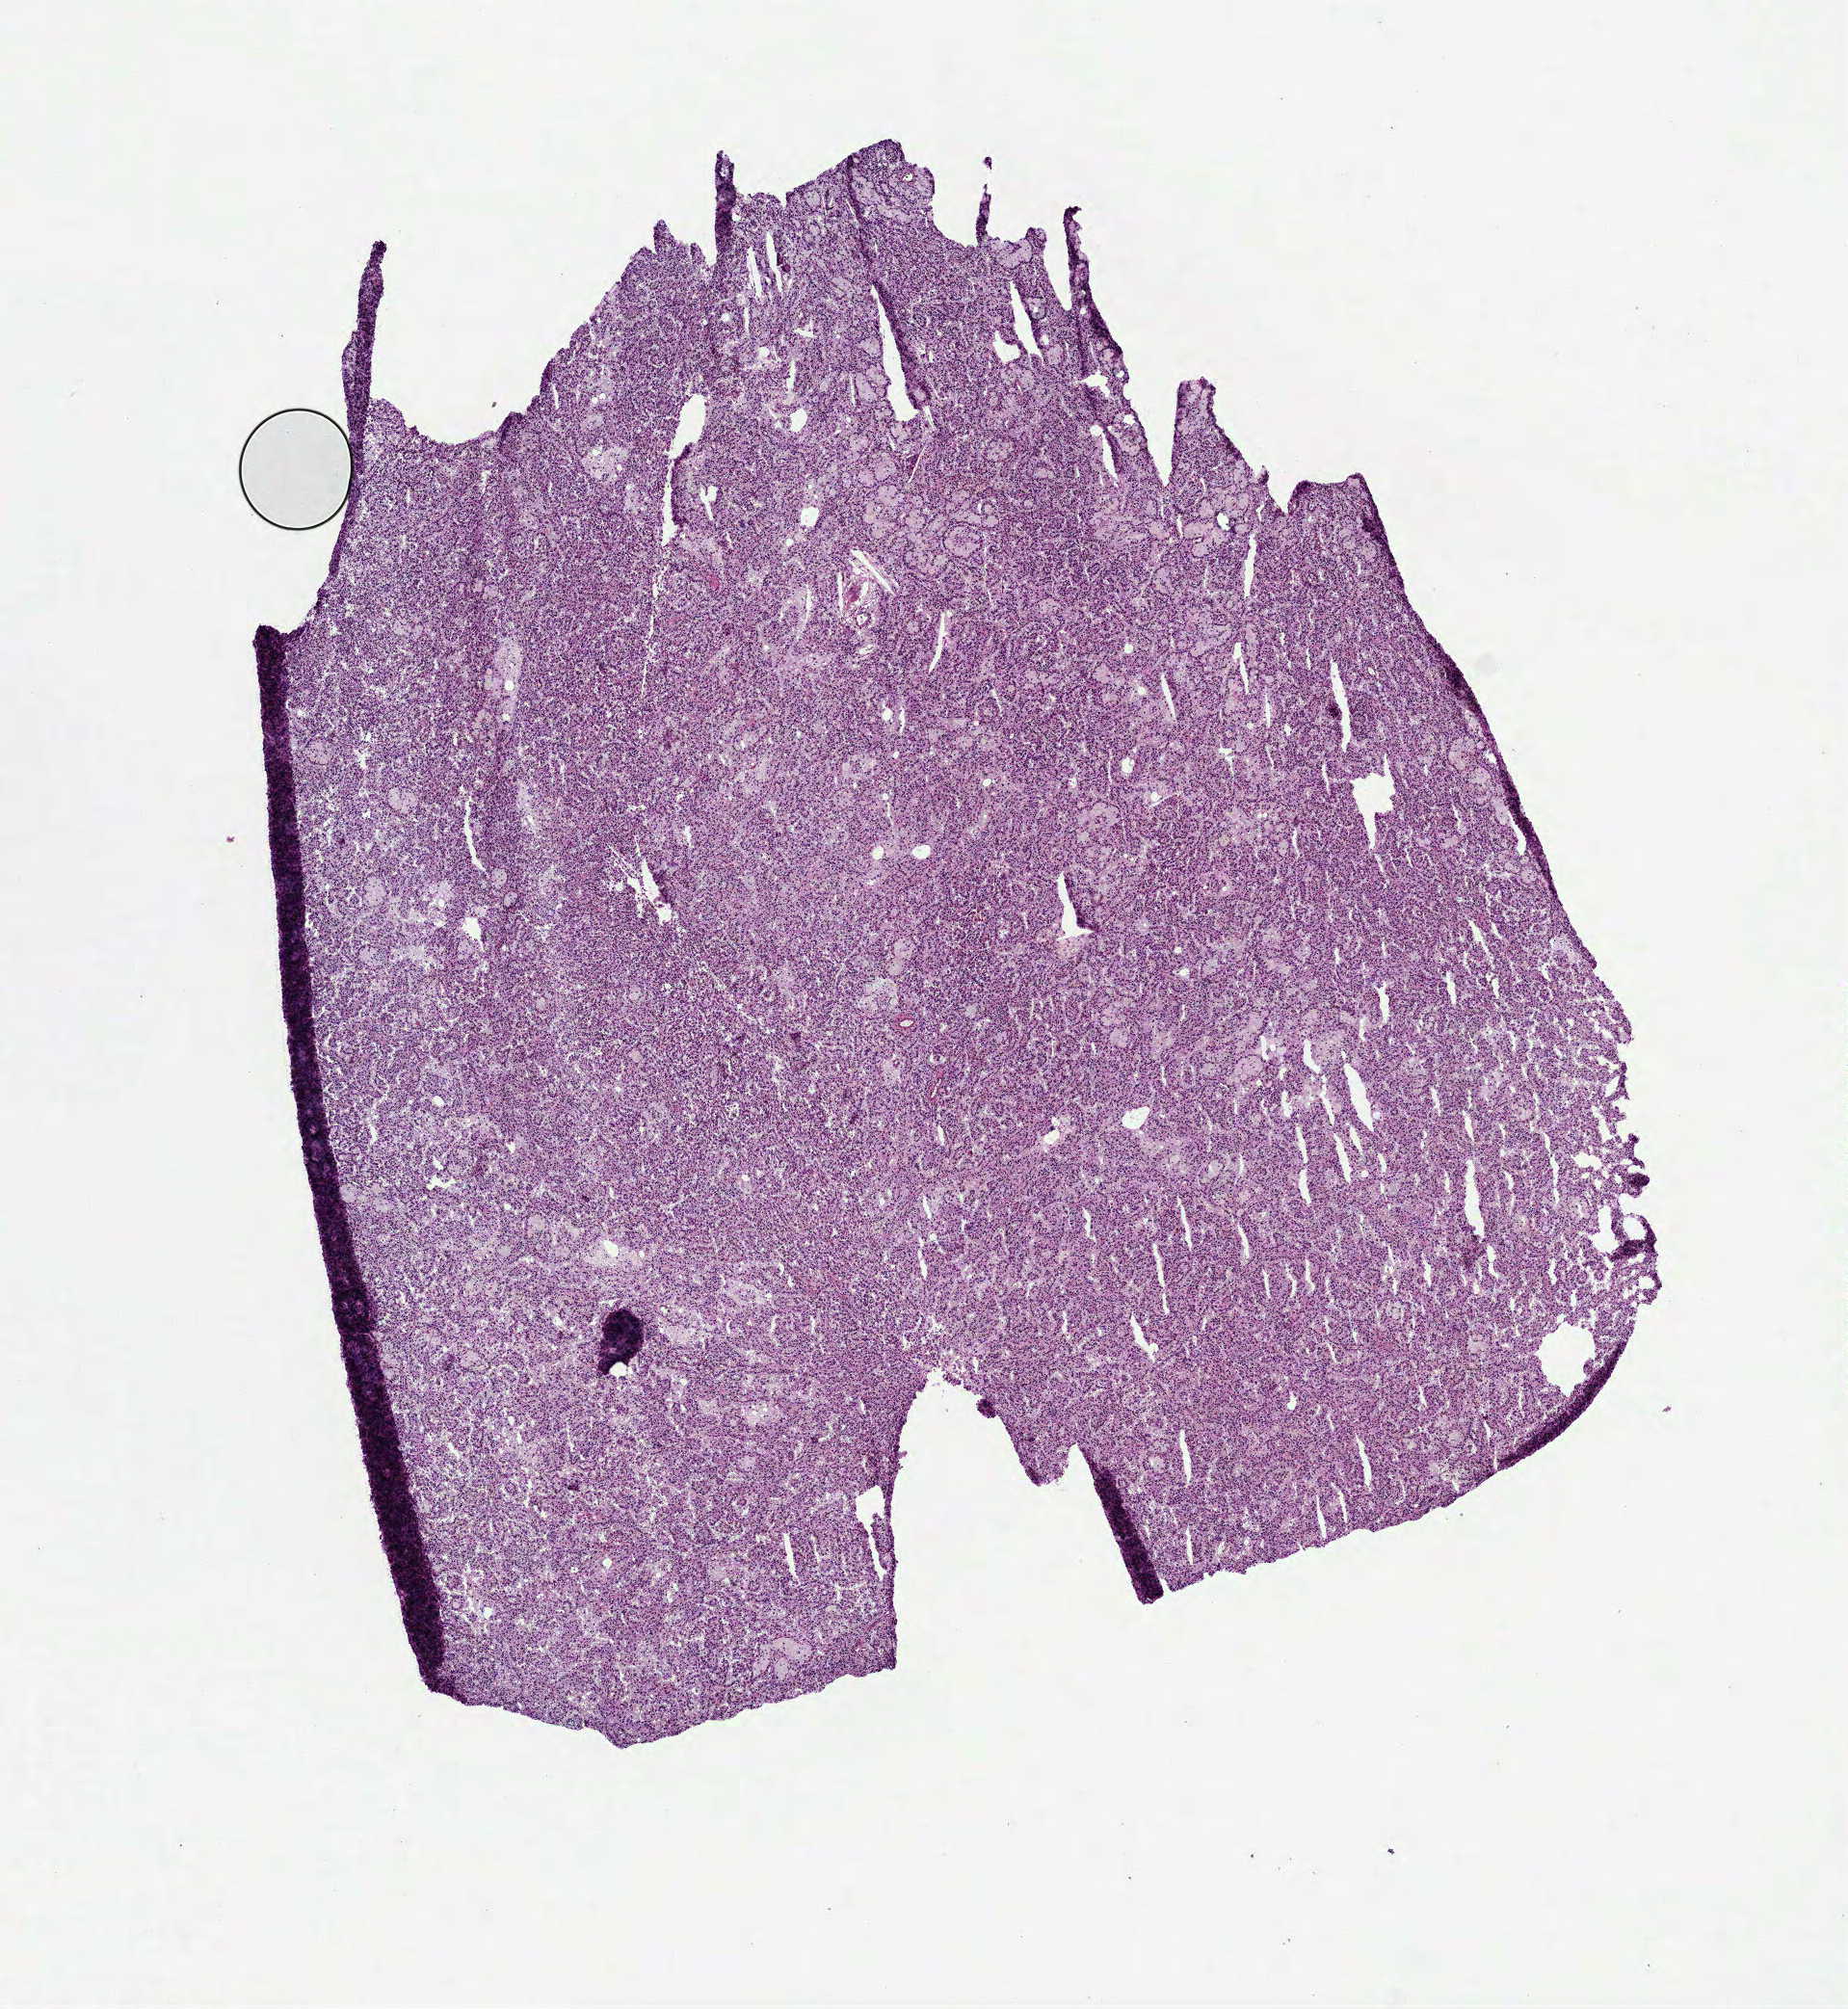
Hematoxylin and eosin (H&E) stained whole-slide image, whole scanned area (about 7.7 x 8.4 mm, from a 40x scan) shown as a low-resolution overview; frozen section; primary tumour sample from the kidney. Patient: male, age at initial diagnosis 57 years. Composition of this section per pathologist review: tumour cells 95%, tumour nuclei 80%, normal cells 0%, stromal cells 5%, necrosis 0%. Inflammatory infiltration, as recorded: lymphocyte infiltration 3%, monocyte infiltration 10%, neutrophil infiltration 0%.
AJCC pathologic stage: I. Histologic diagnosis: Papillary adenocarcinoma, NOS.